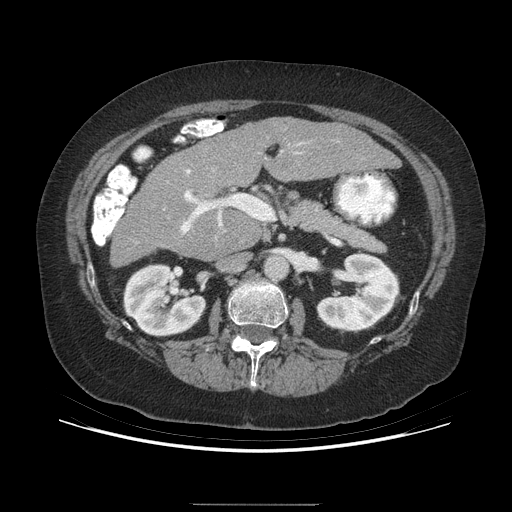
Contrast-enhanced abdominal CT (liver protocol), one axial slice; position 144 of 192 along the scan axis; reconstruction kernel STANDARD; soft-tissue window (W 400 / L 40 HU); 512 × 512 image matrix, field of view 400 × 400 mm. From the clinical record (not read from this slice): diagnosis: hepatocellular carcinoma (patient treated with transarterial chemoembolisation; whether this scan precedes or follows treatment is not stated here); TNM stage (as recorded): Stage-I; Child-Pugh class: A; tumour differentiation: moderately differentiated; tumour nodularity: uninodular.
Structures marked on this image (semi-automatically segmented with operator editing):
- liver parenchyma outside the tumour (the mass and vessels are separate outlines, so this box may not span the whole liver): box from (x=111, y=118) to (x=398, y=266) px
- liver vessels: (x=183, y=143)–(x=302, y=234)